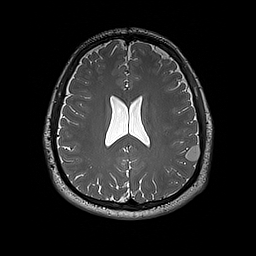
Brain MRI from a brain-tumour surgery series, one axial slice; slice 79 of 192 in the series (ordered by position); 1 mm slice thickness; 256 × 256 image matrix. From the clinical record (not read from this slice): histopathology: Dysembryoplastic neuroepithelial tumor; WHO grade: 1; IDH mutation: no; tumour location: Left Inferior Parietal.
Outlined on this slice (outlined manually by an expert reader):
- tumour: bounding box [x1, y1, x2, y2] px = [185, 146, 200, 161]